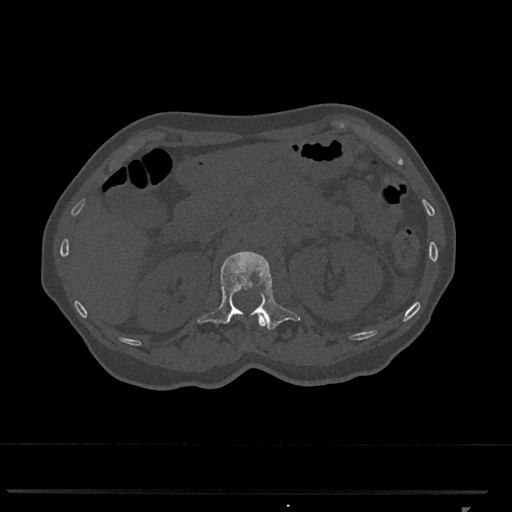
CT including the spine, one axial slice; slice 412 of 793 in the series (ordered by position); bone window (W 1800 / L 400 HU); 512 × 512 image matrix. Patient: female, 62 years. Case-level facts recorded for this patient, not image findings: primary cancer: renal.
Annotated regions visible in this slice (semi-automatically segmented with operator editing):
- L1 vertebra: bounding box [x1, y1, x2, y2] px = [198, 251, 300, 330]
- T12 vertebra: [258, 316, 265, 327]